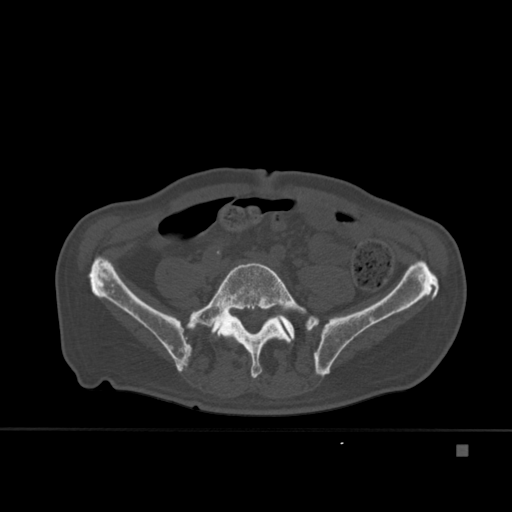
CT including the spine, one axial slice. Position 103 of 451 along the scan axis. Bone window (W 1800 / L 400 HU). 512 × 512 image matrix. Patient: male, 75 years. From the clinical record (not read from this slice): primary cancer: prostate.
Structures marked on this image (semi-automatic segmentation, software-assisted and operator-edited):
- L4 vertebra: box from (x=225, y=336) to (x=231, y=339) px
- L5 vertebra: (x=186, y=262)–(x=307, y=378)
- T7 vertebra: (x=210, y=295)–(x=246, y=329)